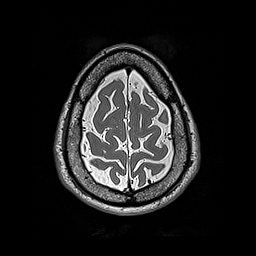
Brain MRI from a brain-tumour surgery series, one axial slice. 1 mm slice thickness. 256 × 256 image matrix, field of view 250 × 250 mm. Case-level facts recorded for this patient, not image findings: histopathology: Astrocytoma; WHO grade: 2; IDH mutation: yes; tumour location: Left Frontal.
Structures marked on this image (outlined manually by an expert reader):
- tumour: bounding box [x1, y1, x2, y2] px = [161, 111, 166, 121]